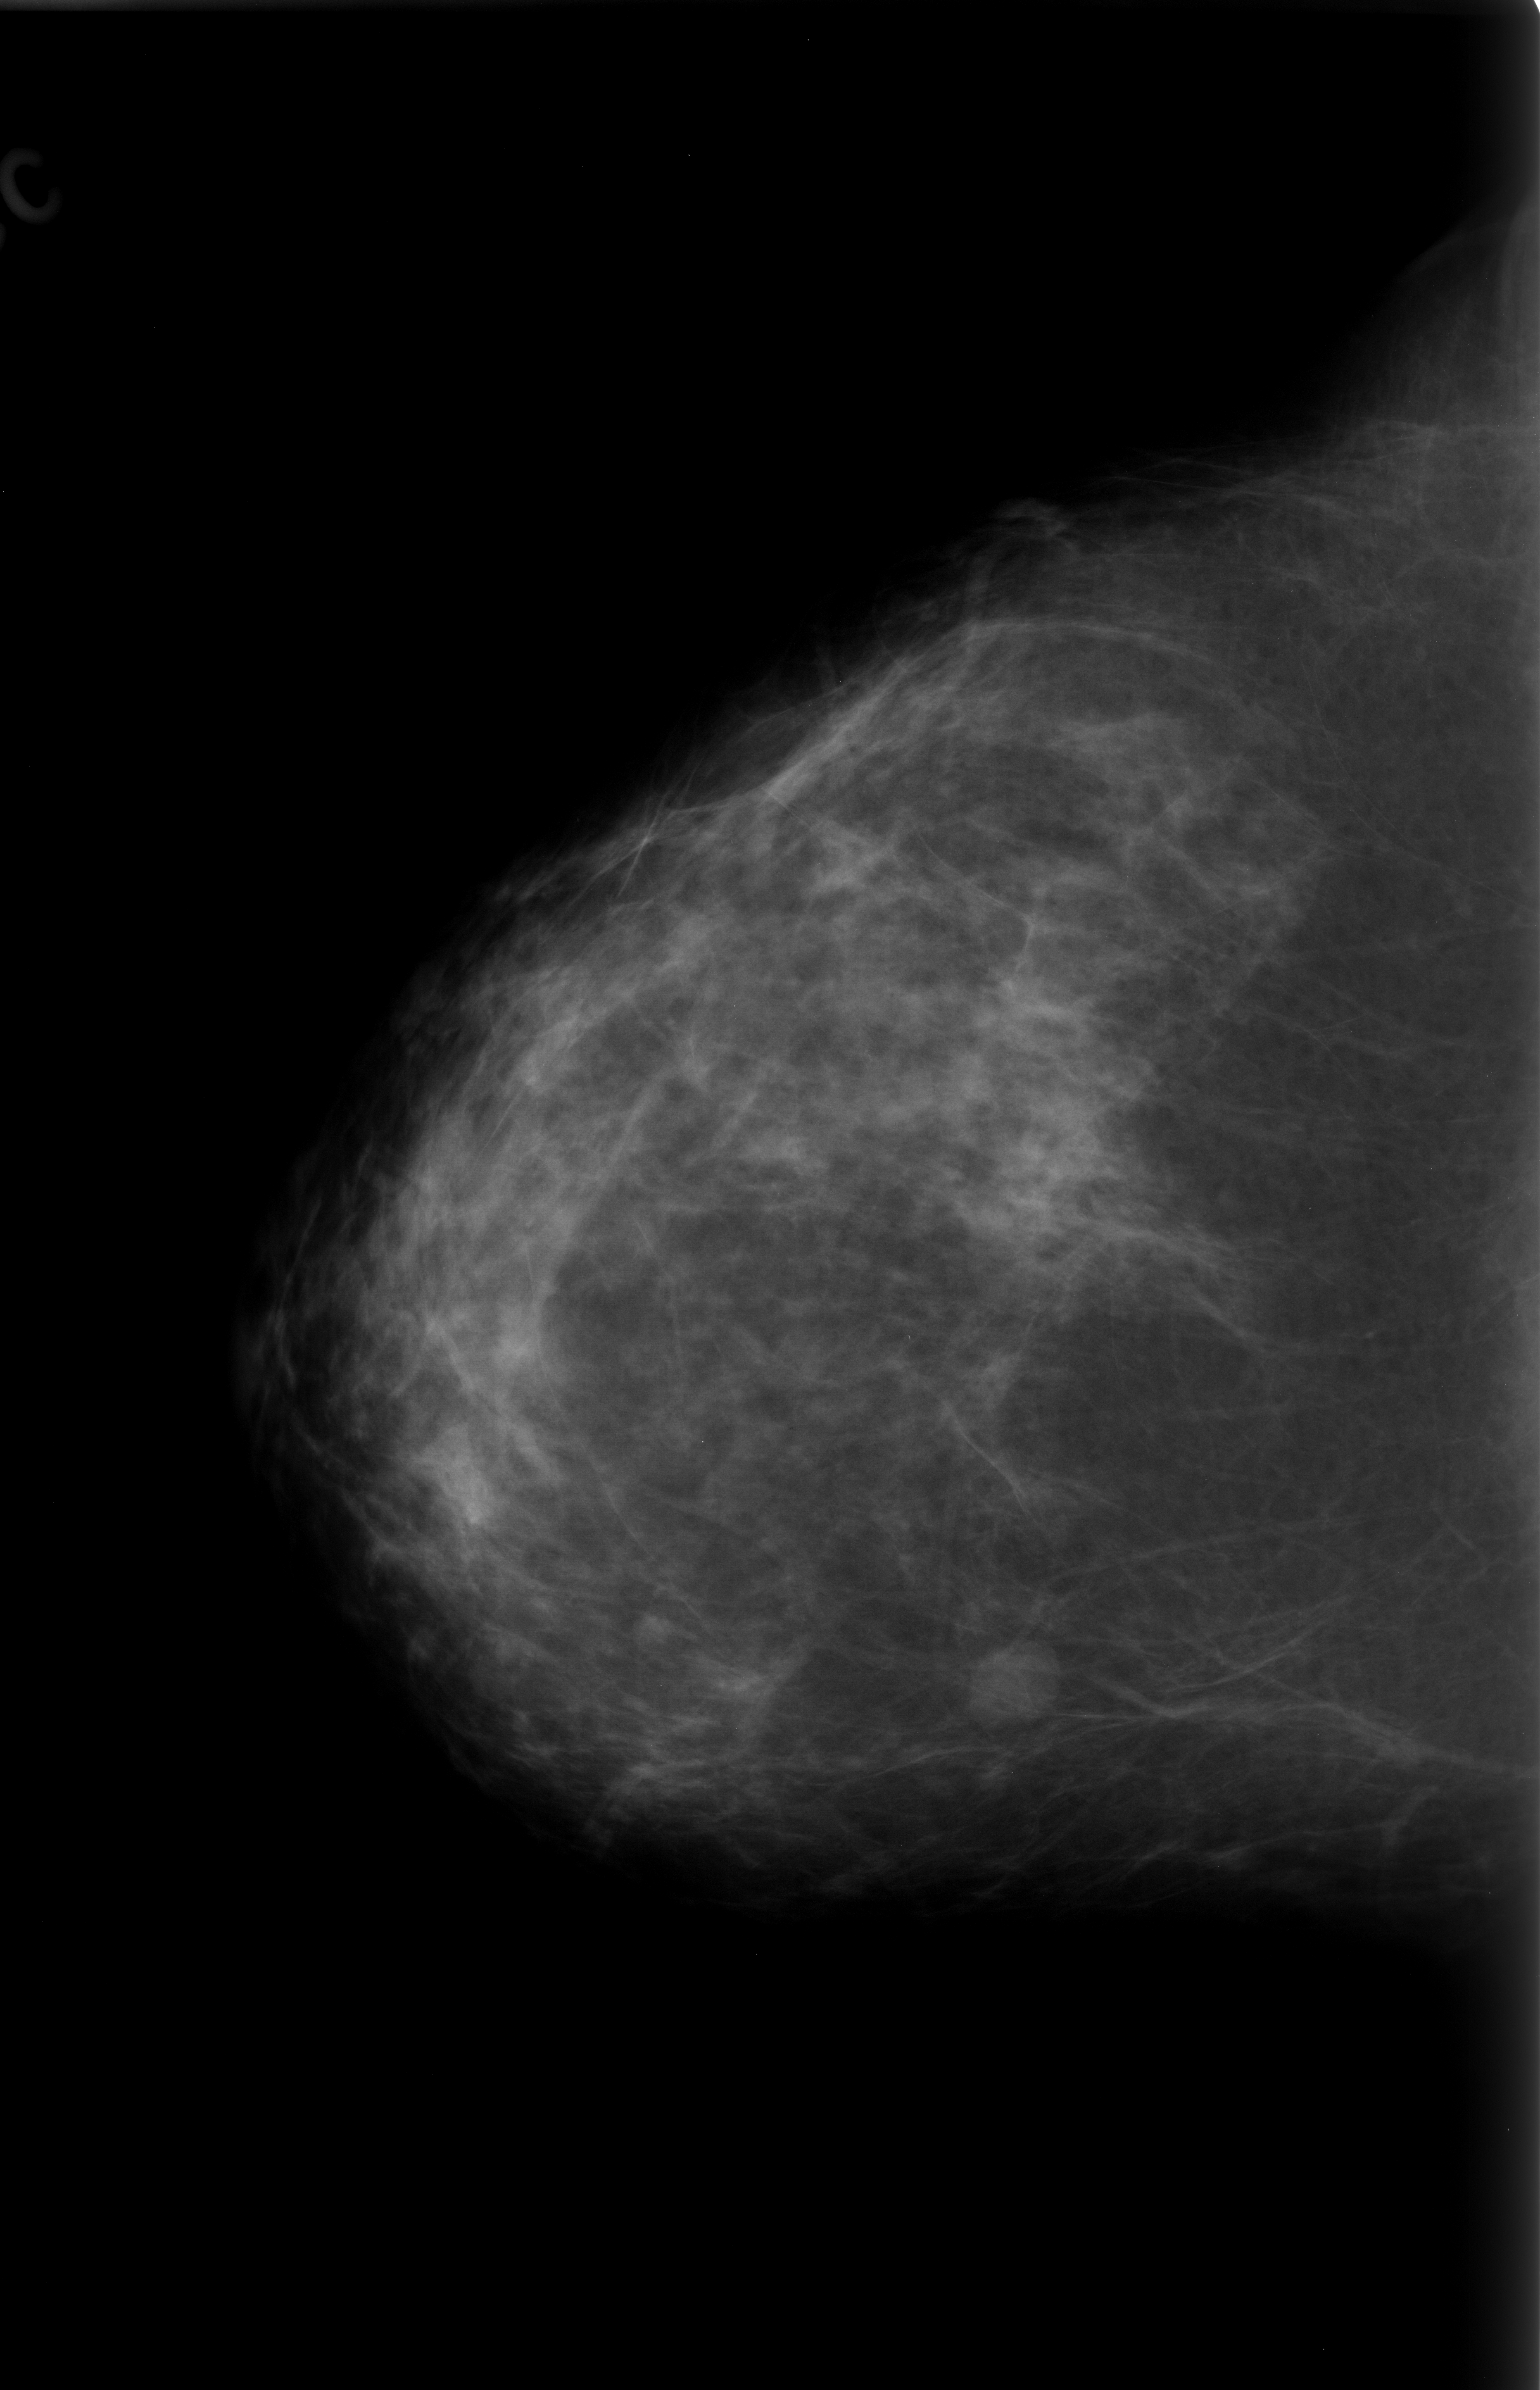
Digitized screen-film mammogram; right breast; craniocaudal (CC) view; breast composition: scattered fibroglandular densities (BI-RADS density category 2 of 4).
Finding: mass, shape oval, margins circumscribed; BI-RADS assessment category 3; pathology (as recorded): benign.